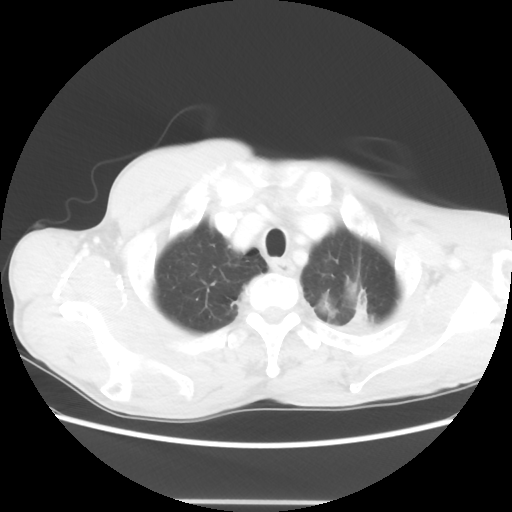
Chest CT, one axial slice; slice 58 of 62 in the series (ordered by position); reconstruction kernel STANDARD; lung window (W 1500 / L -600 HU); 512 × 512 image matrix, field of view 360 × 360 mm. Patient: male, 61 years. Case-level facts recorded for this patient, not image findings: clinical TNM (as recorded): T3 N1 M1.
Structures marked on this image (rectangle marked by the reading radiologist):
- lung tumour (recorded histology: adenocarcinoma): box from (x=351, y=301) to (x=381, y=337) px